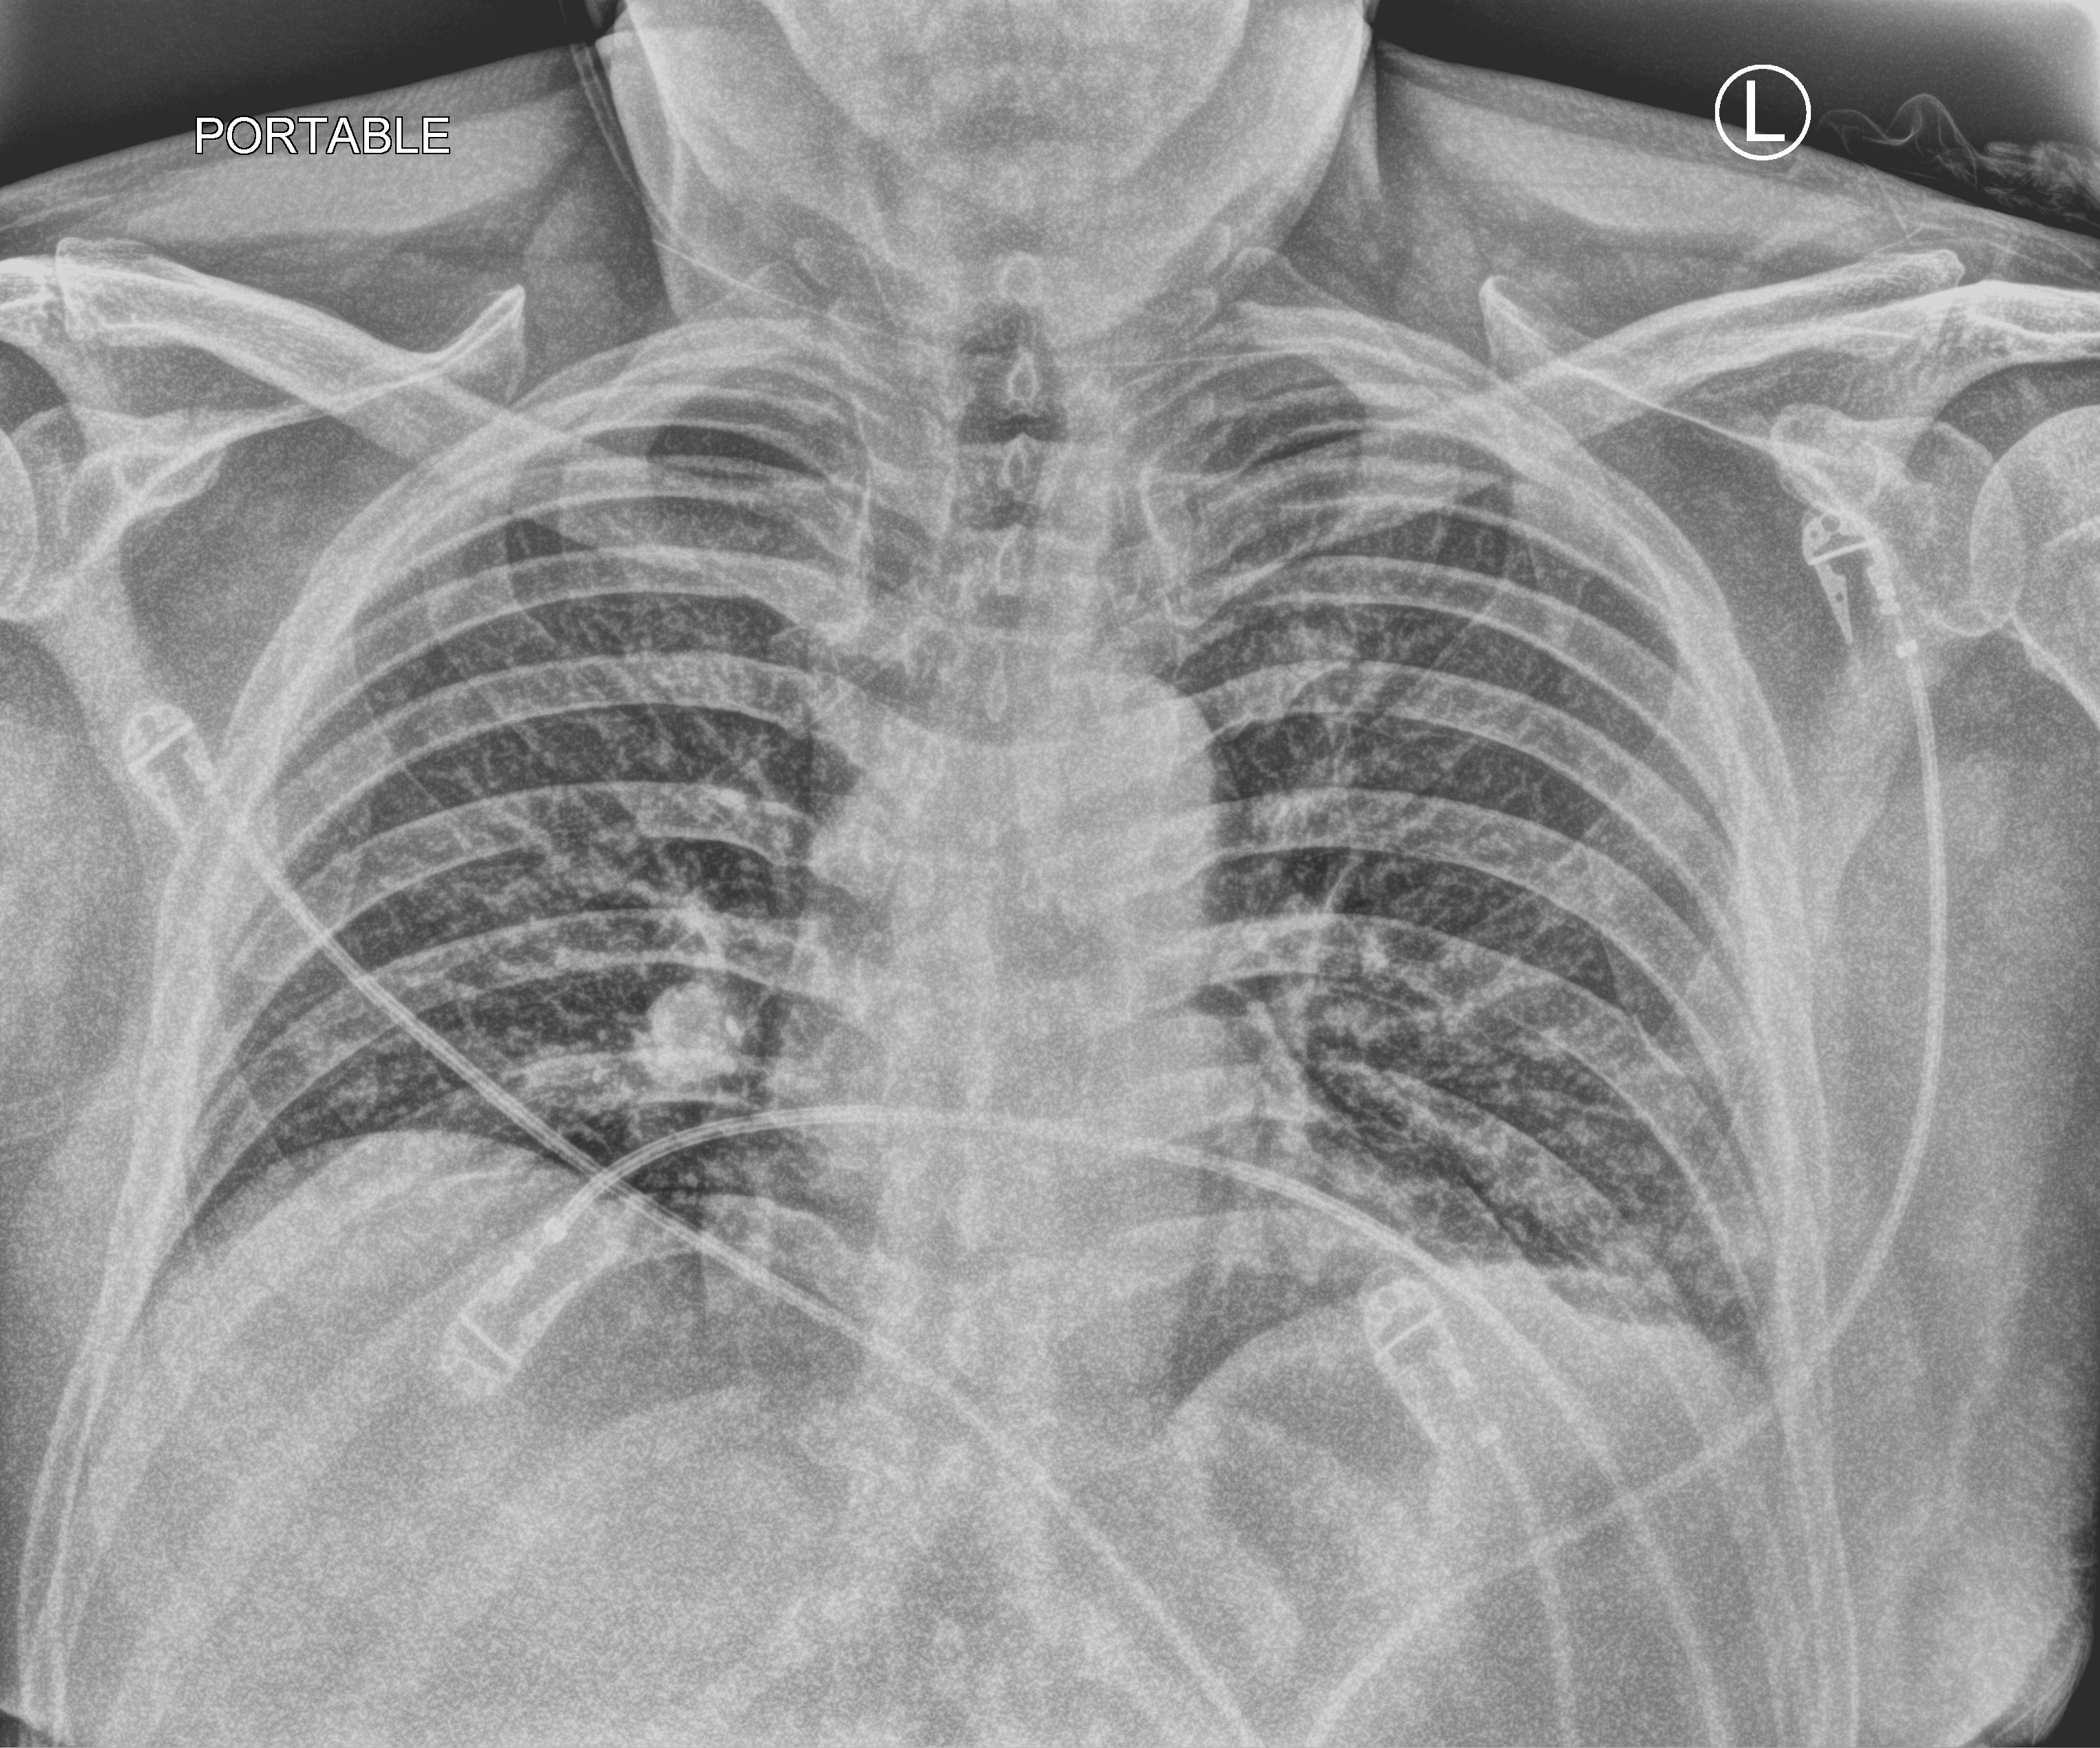
Bedside chest radiograph (computed radiography). Patient hospitalised with COVID-19; male, aged 60–74 years.
Hospital-stay facts (about this admission, not read from this image; timing relative to this image not recorded): COPD (admission record): no; other chronic lung disease (admission record): no; mechanically ventilated during this hospital stay: no.